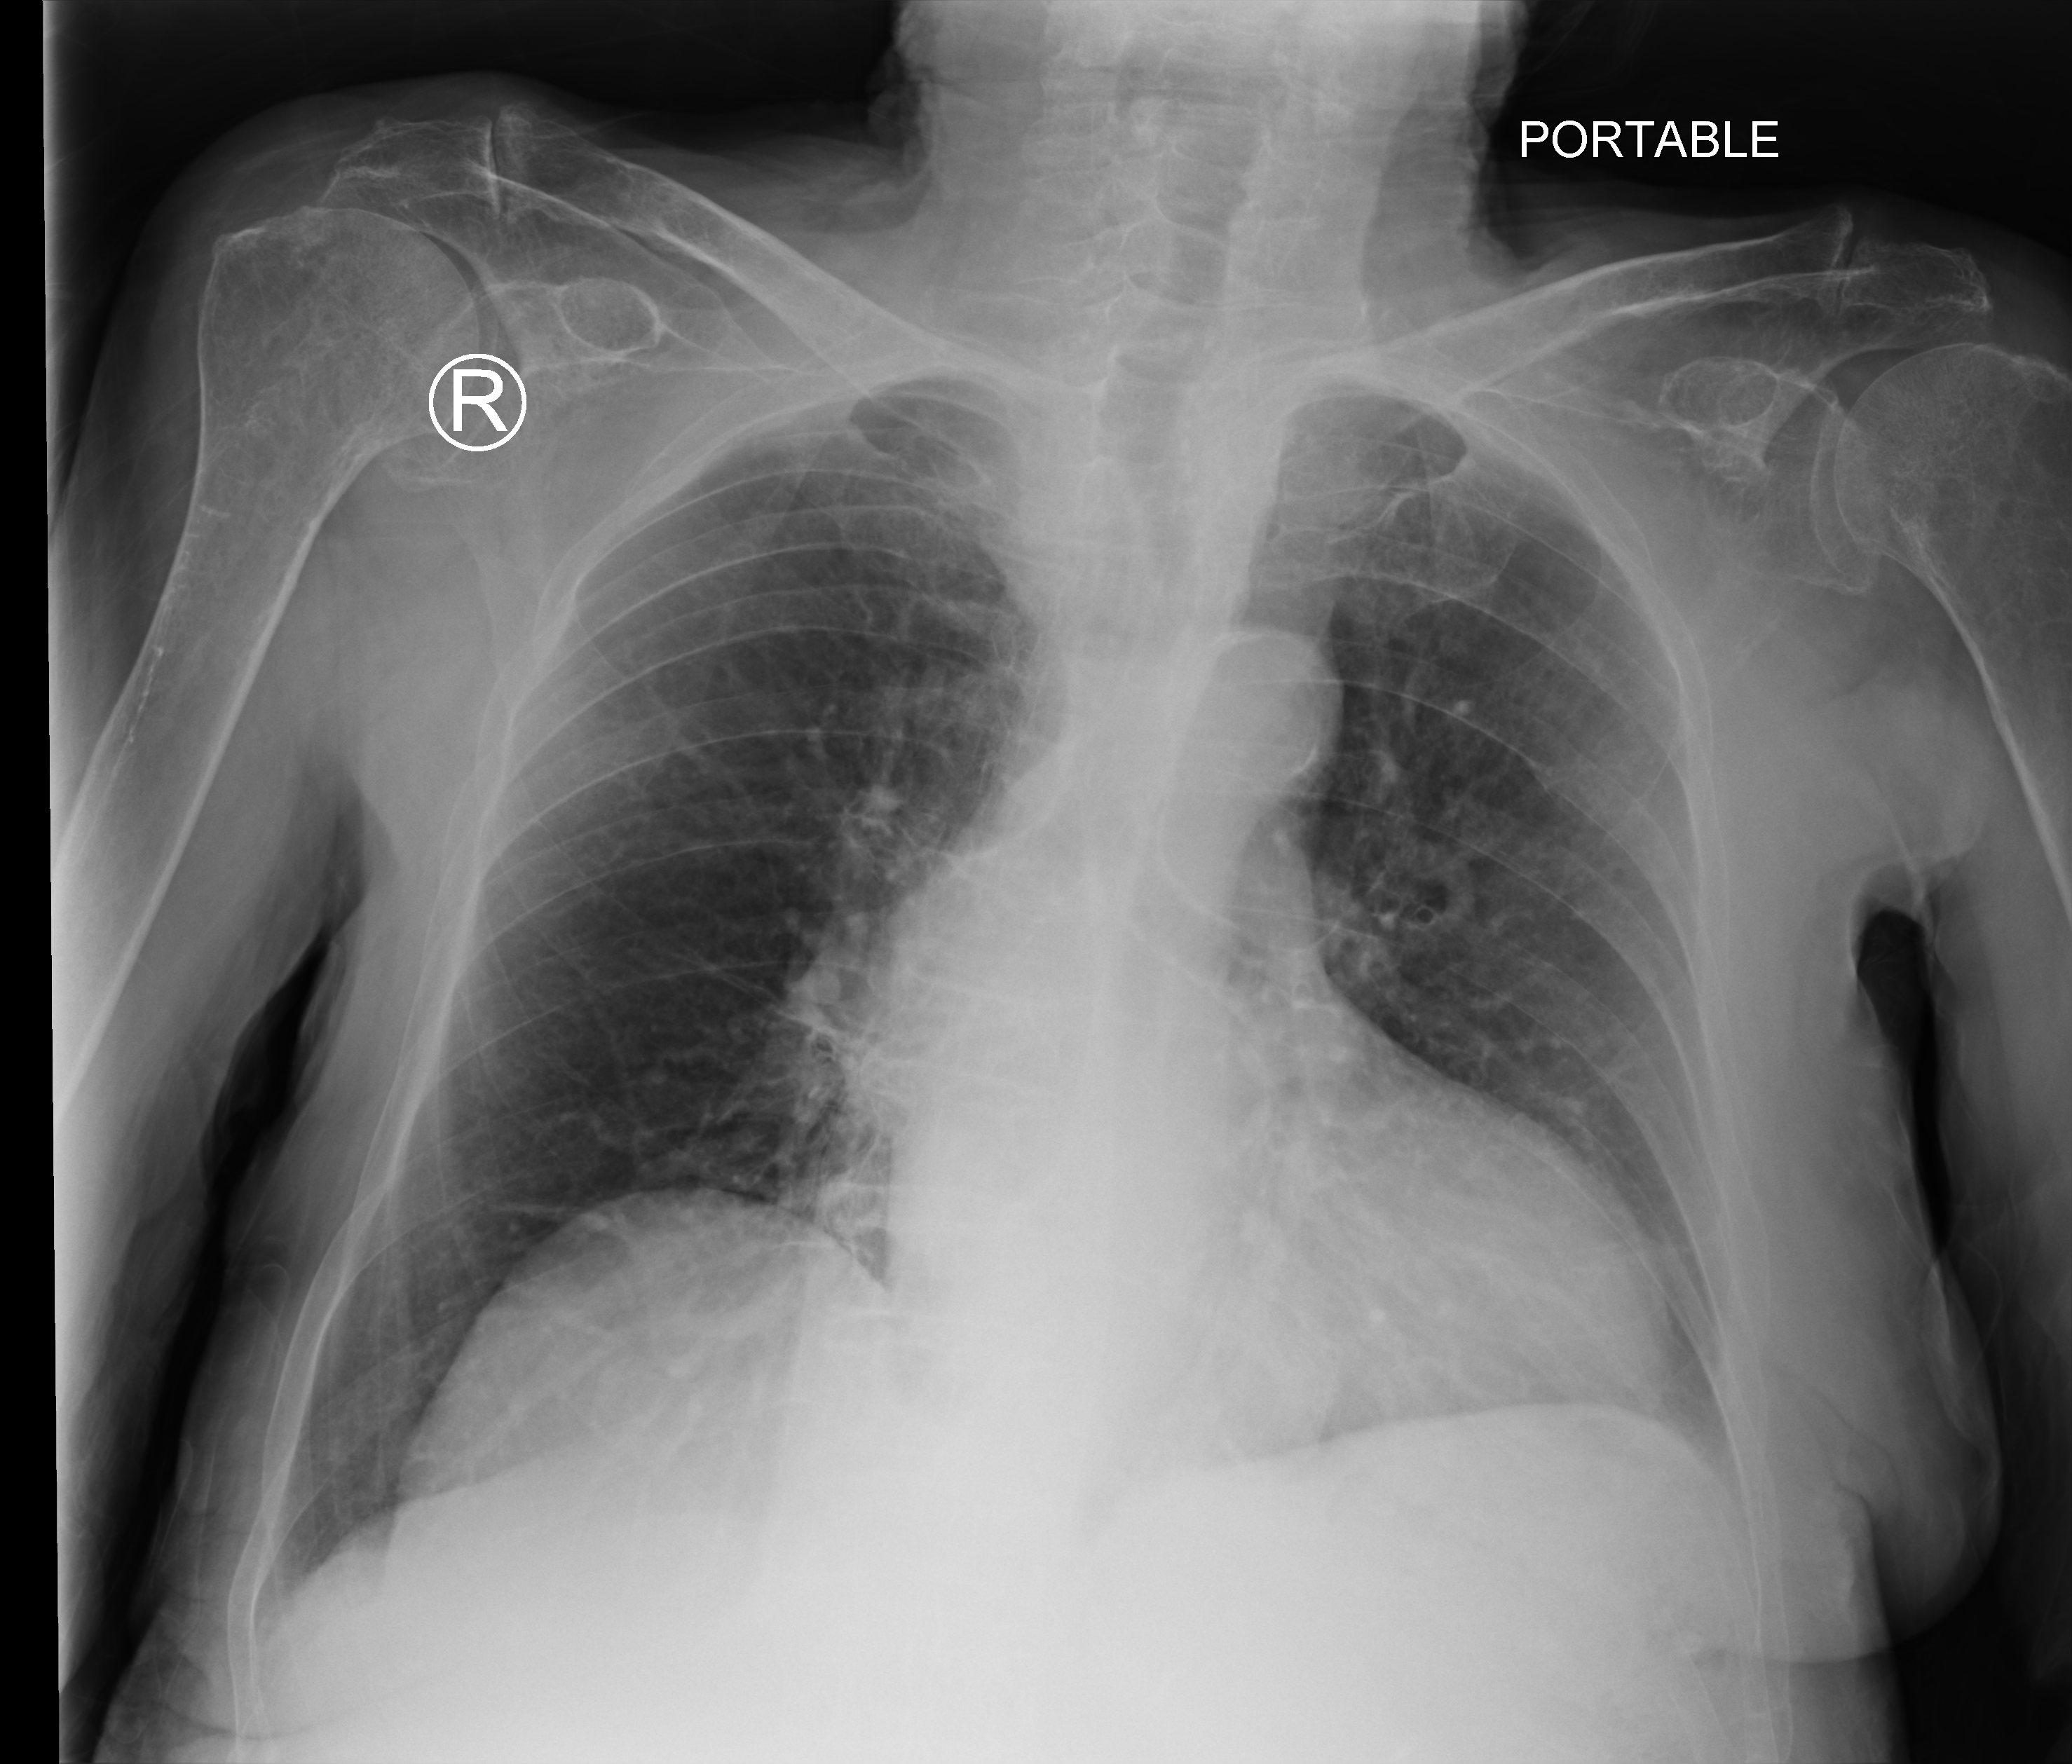
Chest X-ray (portable), anteroposterior (AP) projection. Female patient hospitalised with COVID-19, age 75–90 years.
Hospital-stay facts (about this admission, not read from this image; timing relative to this image not recorded):
- admitted to intensive care during this hospital stay: no
- mechanically ventilated during this hospital stay: no